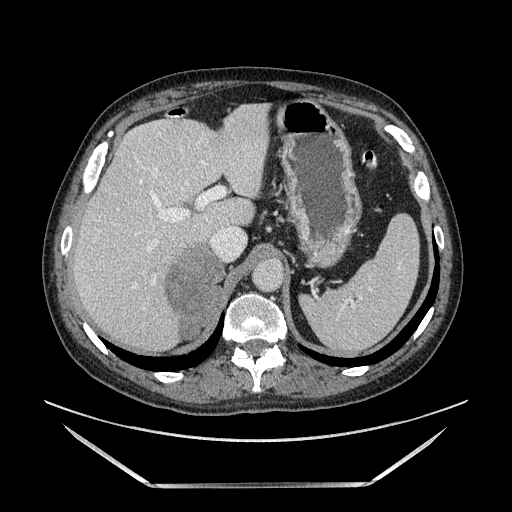
Contrast-enhanced abdominal CT, one axial slice. Position 105 of 185 along the scan axis. Soft-tissue window (W 400 / L 40 HU). 512 × 512 image matrix, field of view 440 × 440 mm. Male patient. From the clinical record (not read from this slice): diagnosis: adrenocortical carcinoma; tumour side: right adrenal; tumour size at pathology: 10.3 cm; Ki-67 index: 20 %; stage (as recorded): 3.
Annotated regions visible in this slice (semi-automatic segmentation, software-assisted and operator-edited):
- mass: bounding box (x1, y1, x2, y2) in pixels: (166, 246, 223, 337)